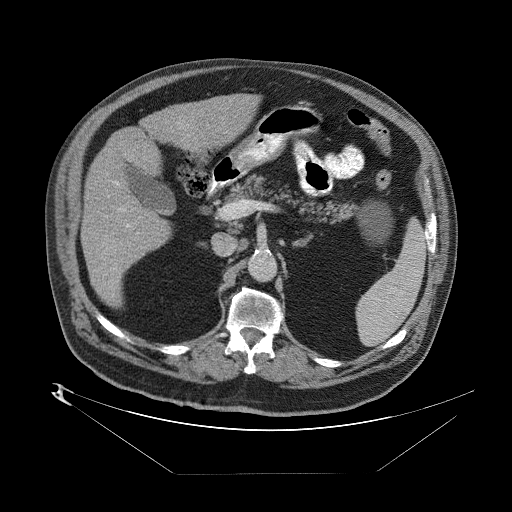
Contrast-enhanced abdominal CT (liver protocol), one axial slice; position 36 of 89 along the scan axis; 140 kVp; one of 2 acquisitions stored at this slice position; soft-tissue window (W 400 / L 40 HU); 2.5 mm slice thickness; 512 × 512 image matrix, field of view 480 × 480 mm. From the clinical record (not read from this slice): diagnosis: hepatocellular carcinoma (patient treated with transarterial chemoembolisation; whether this scan precedes or follows treatment is not stated here); TNM stage (as recorded): Stage-II; Child-Pugh class: B.
Structures marked on this image (semi-automatically segmented with operator editing):
- abdominal aorta: box from (x=250, y=254) to (x=275, y=280) px
- liver parenchyma outside the tumour (the mass and vessels are separate outlines, so this box may not span the whole liver): (x=82, y=92)–(x=258, y=312)
- liver vessels: (x=104, y=192)–(x=140, y=267)